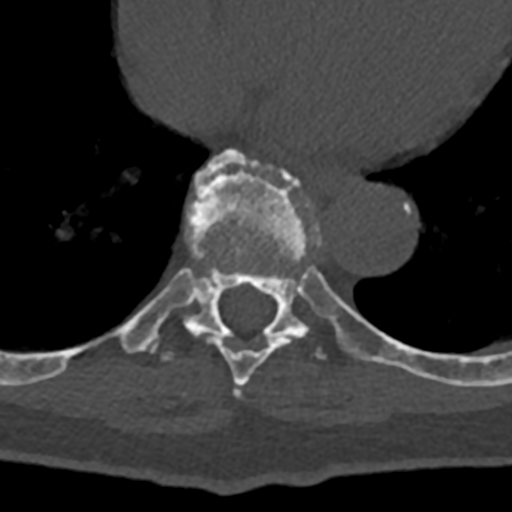
CT including the spine, one axial slice; reconstruction kernel Br40s/3; 120 kVp; bone window (W 1800 / L 400 HU); 0.5 mm slice thickness; 512 × 512 image matrix. Patient: male, 74 years. From the clinical record (not read from this slice): primary cancer: renal.
Structures marked on this image (semi-automatically segmented with operator editing):
- T7 vertebra: bounding box [x1, y1, x2, y2] px = [234, 385, 241, 398]
- T8 vertebra: [71, 274, 339, 386]
- T9 vertebra: [86, 149, 432, 379]